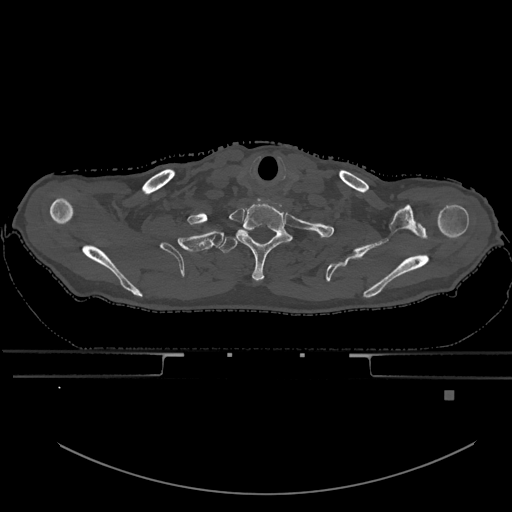
CT including the spine, one axial slice. Position 568 of 969 along the scan axis. Bone window (W 1800 / L 400 HU). 0.5 mm slice thickness. 512 × 512 image matrix, field of view 456 × 456 mm. Patient: male, 82 years. From the clinical record (not read from this slice): primary cancer: prostate; vertebrae with lytic lesions (as recorded): T11, T9, T8, T2.
Structures marked on this image (semi-automatically segmented with operator editing):
- T1 vertebra: bounding box <219,238,239,253> (left, top, right, bottom; pixels)